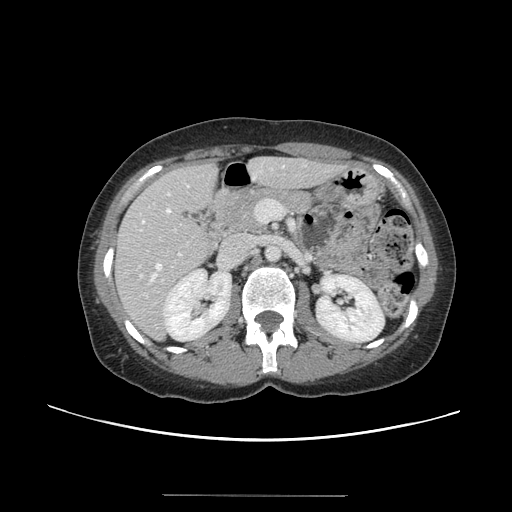
Contrast-enhanced abdominal CT, one axial slice; slice 68 of 144 in the series (ordered by position); 120 kVp; intravenous contrast given; soft-tissue window (W 400 / L 40 HU); 2.5 mm slice thickness; 512 × 512 image matrix, field of view 380 × 380 mm. Female patient, age 53 years. Case-level facts recorded for this patient, not image findings: diagnosis: colorectal cancer liver metastases, imaged before liver resection; multiple liver metastases: yes; largest metastasis: 1.1 cm; chemotherapy before resection: no.
Structures marked on this image (outlined manually by an expert reader):
- hepatic veins: box from (x=140, y=193) to (x=171, y=279) px
- liver: (x=118, y=159)–(x=337, y=338)
- planned liver remnant (the part of the liver to remain after resection): (x=118, y=159)–(x=324, y=304)
- portal vein (with intrahepatic branches): (x=139, y=199)–(x=285, y=297)